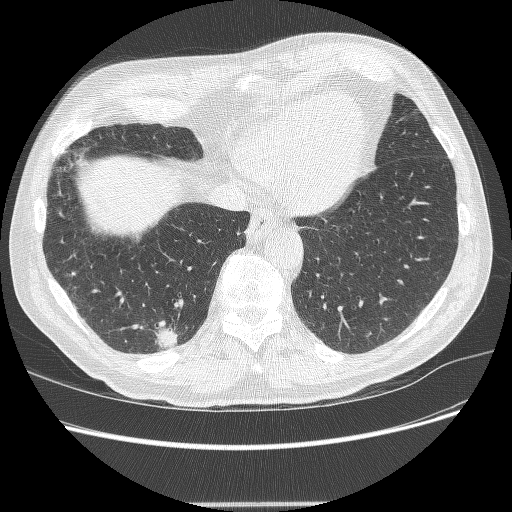
Chest CT (low-dose screening protocol), one axial image. Second screening round (one year after baseline). Lung window (W 1500 / L -600 HU). 1.25 mm slice thickness. 120 kVp. 512 × 512 image matrix, field of view 372 × 372 mm. Male participant, aged 71 years at enrolment. Current smoker at enrolment.
Lesion marked by an expert reader, bounding box [x1, y1, x2, y2] px = [137, 321, 187, 358]. The screening reader recorded 5 non-calcified nodules or masses ≥4 mm on this exam (right lower lobe, right lower lobe, right upper lobe, right upper lobe, right upper lobe); which of them this box marks is not recorded. Lung cancer was diagnosed 7 days after this screen: squamous cell carcinoma, NOS, right lower lobe, moderately differentiated (G2), stage IA (AJCC 6th edition), 27 mm at pathology.